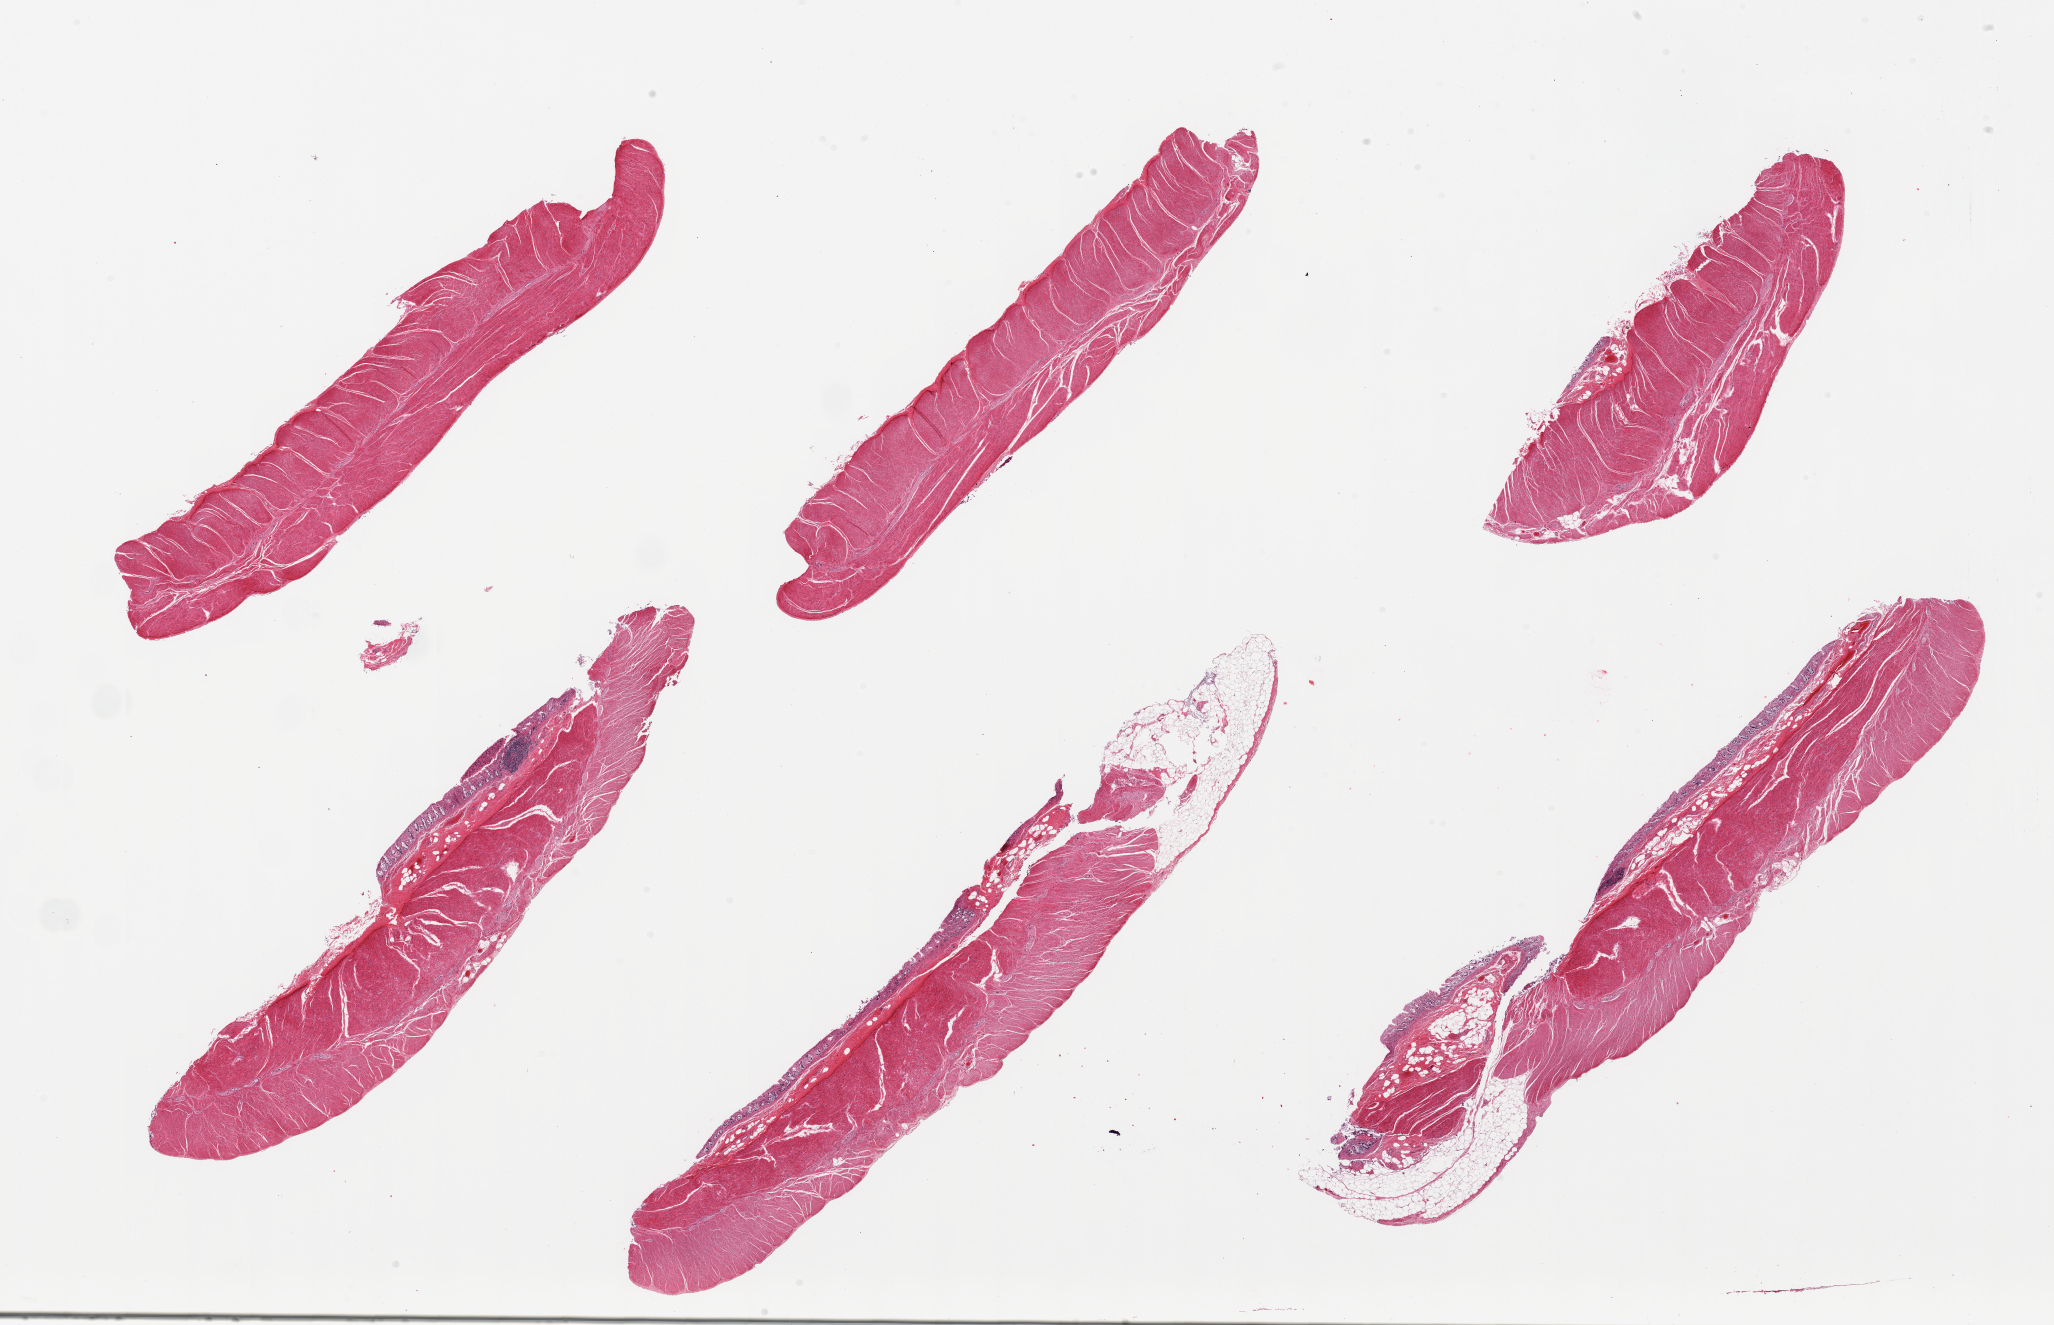
Digitized hematoxylin and eosin (H&E)-stained section, low-resolution overview of the scanned area, about 32.5 x 21.0 mm, PAXgene-fixed paraffin-embedded (PFPE) section, section of sigmoid colon (target tissue), tissue donor sample. Male donor.
Pathologist's review note for this sample: 6 pieces; 4 have autolyzed mucosa (not target).